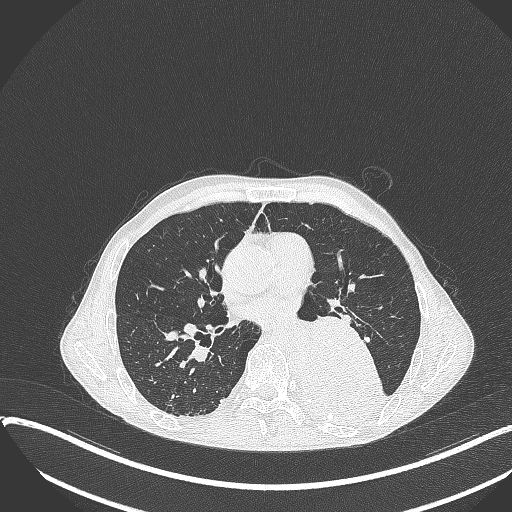
Chest CT, one axial slice; slice 189 of 401 in the series (ordered by position); reconstruction kernel B70f; 120 kVp; lung window (W 1500 / L -600 HU); 1 mm slice thickness; 512 × 512 image matrix, field of view 400 × 400 mm. Male patient, age 57 years. From the clinical record (not read from this slice): clinical TNM (as recorded): T4 N0 M0.
Outlined on this slice (bounding box drawn by a radiologist):
- lung tumour (recorded histology: squamous cell carcinoma): bounding box <289,311,388,428> (left, top, right, bottom; pixels)